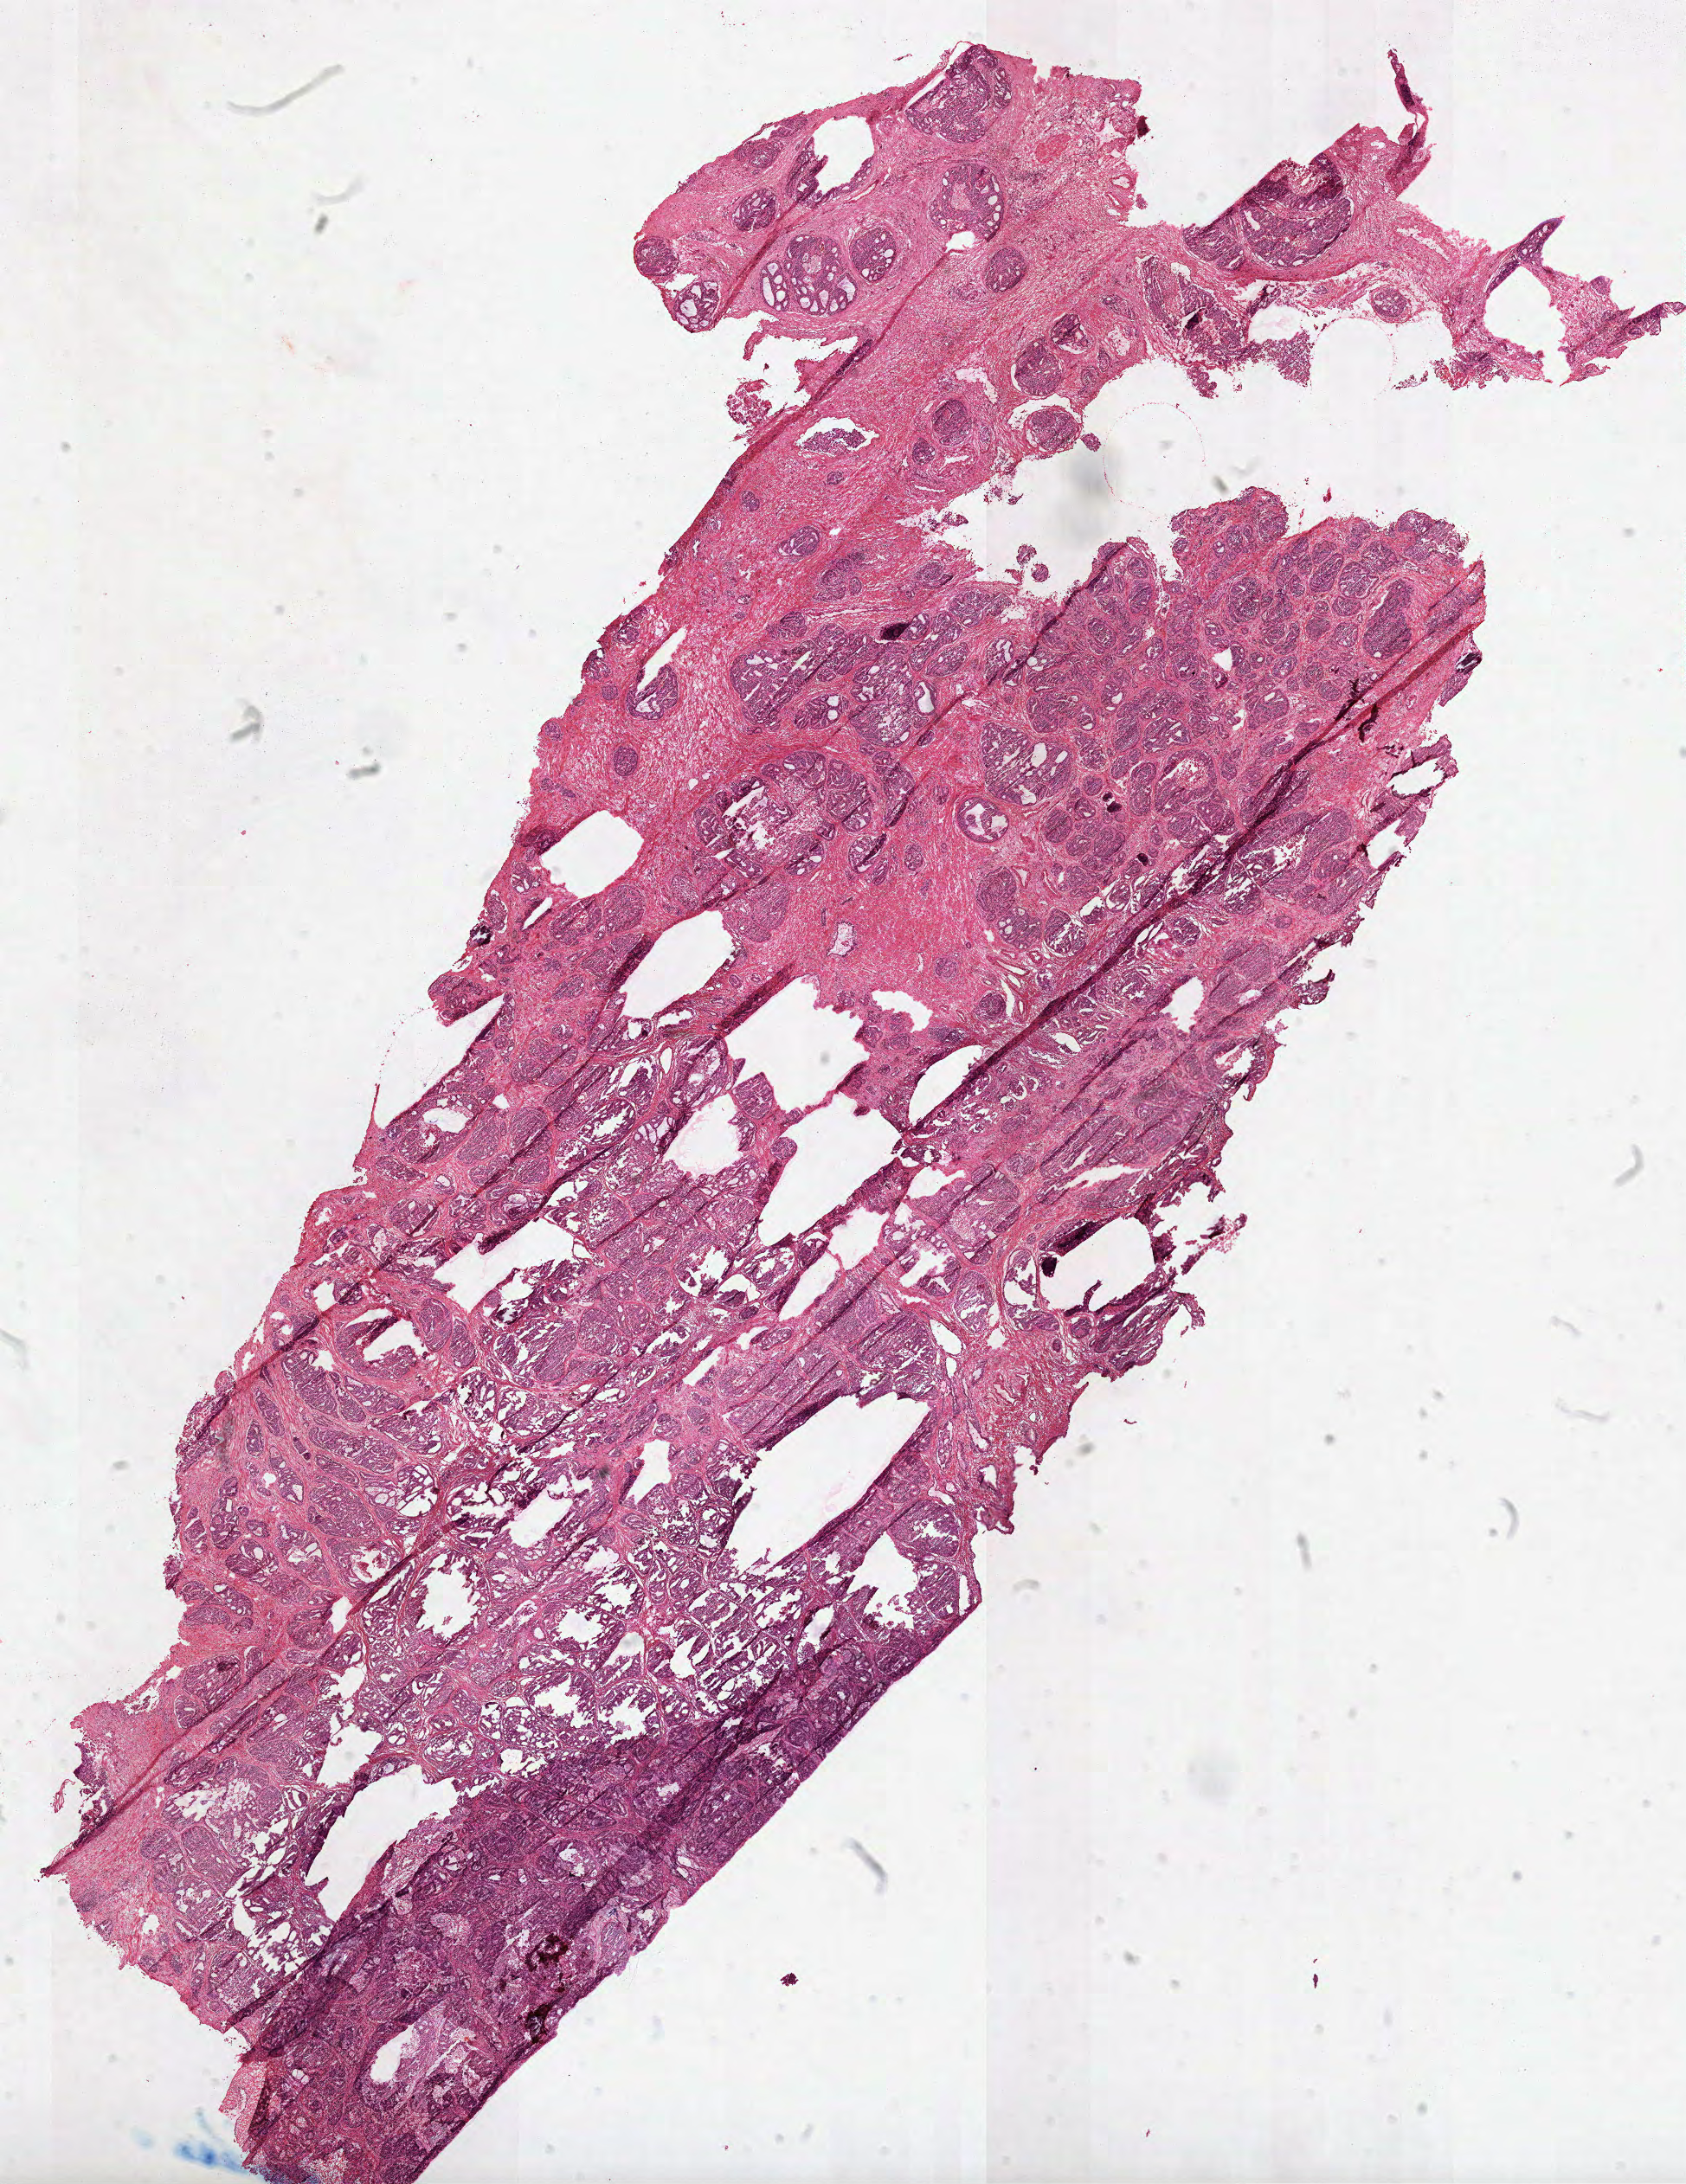
Whole-slide histology image, H&E, whole scanned area (about 15.7 x 20.4 mm, acquisition: 40x scan) shown as a low-resolution overview. Frozen section from the top of the tissue portion. Sample: primary tumour, prostate. Male, age 46 years at initial diagnosis. Gleason score: 9 (4+5). Pathologist review of this section (percent, as recorded): tumour cells 75%, tumour nuclei 75%, normal cells 5%, stromal cells 20%, necrosis 0%.
Lymph nodes positive (case pathology): 0 of 57 examined. Diagnosis: Acinar cell carcinoma (prostate gland).